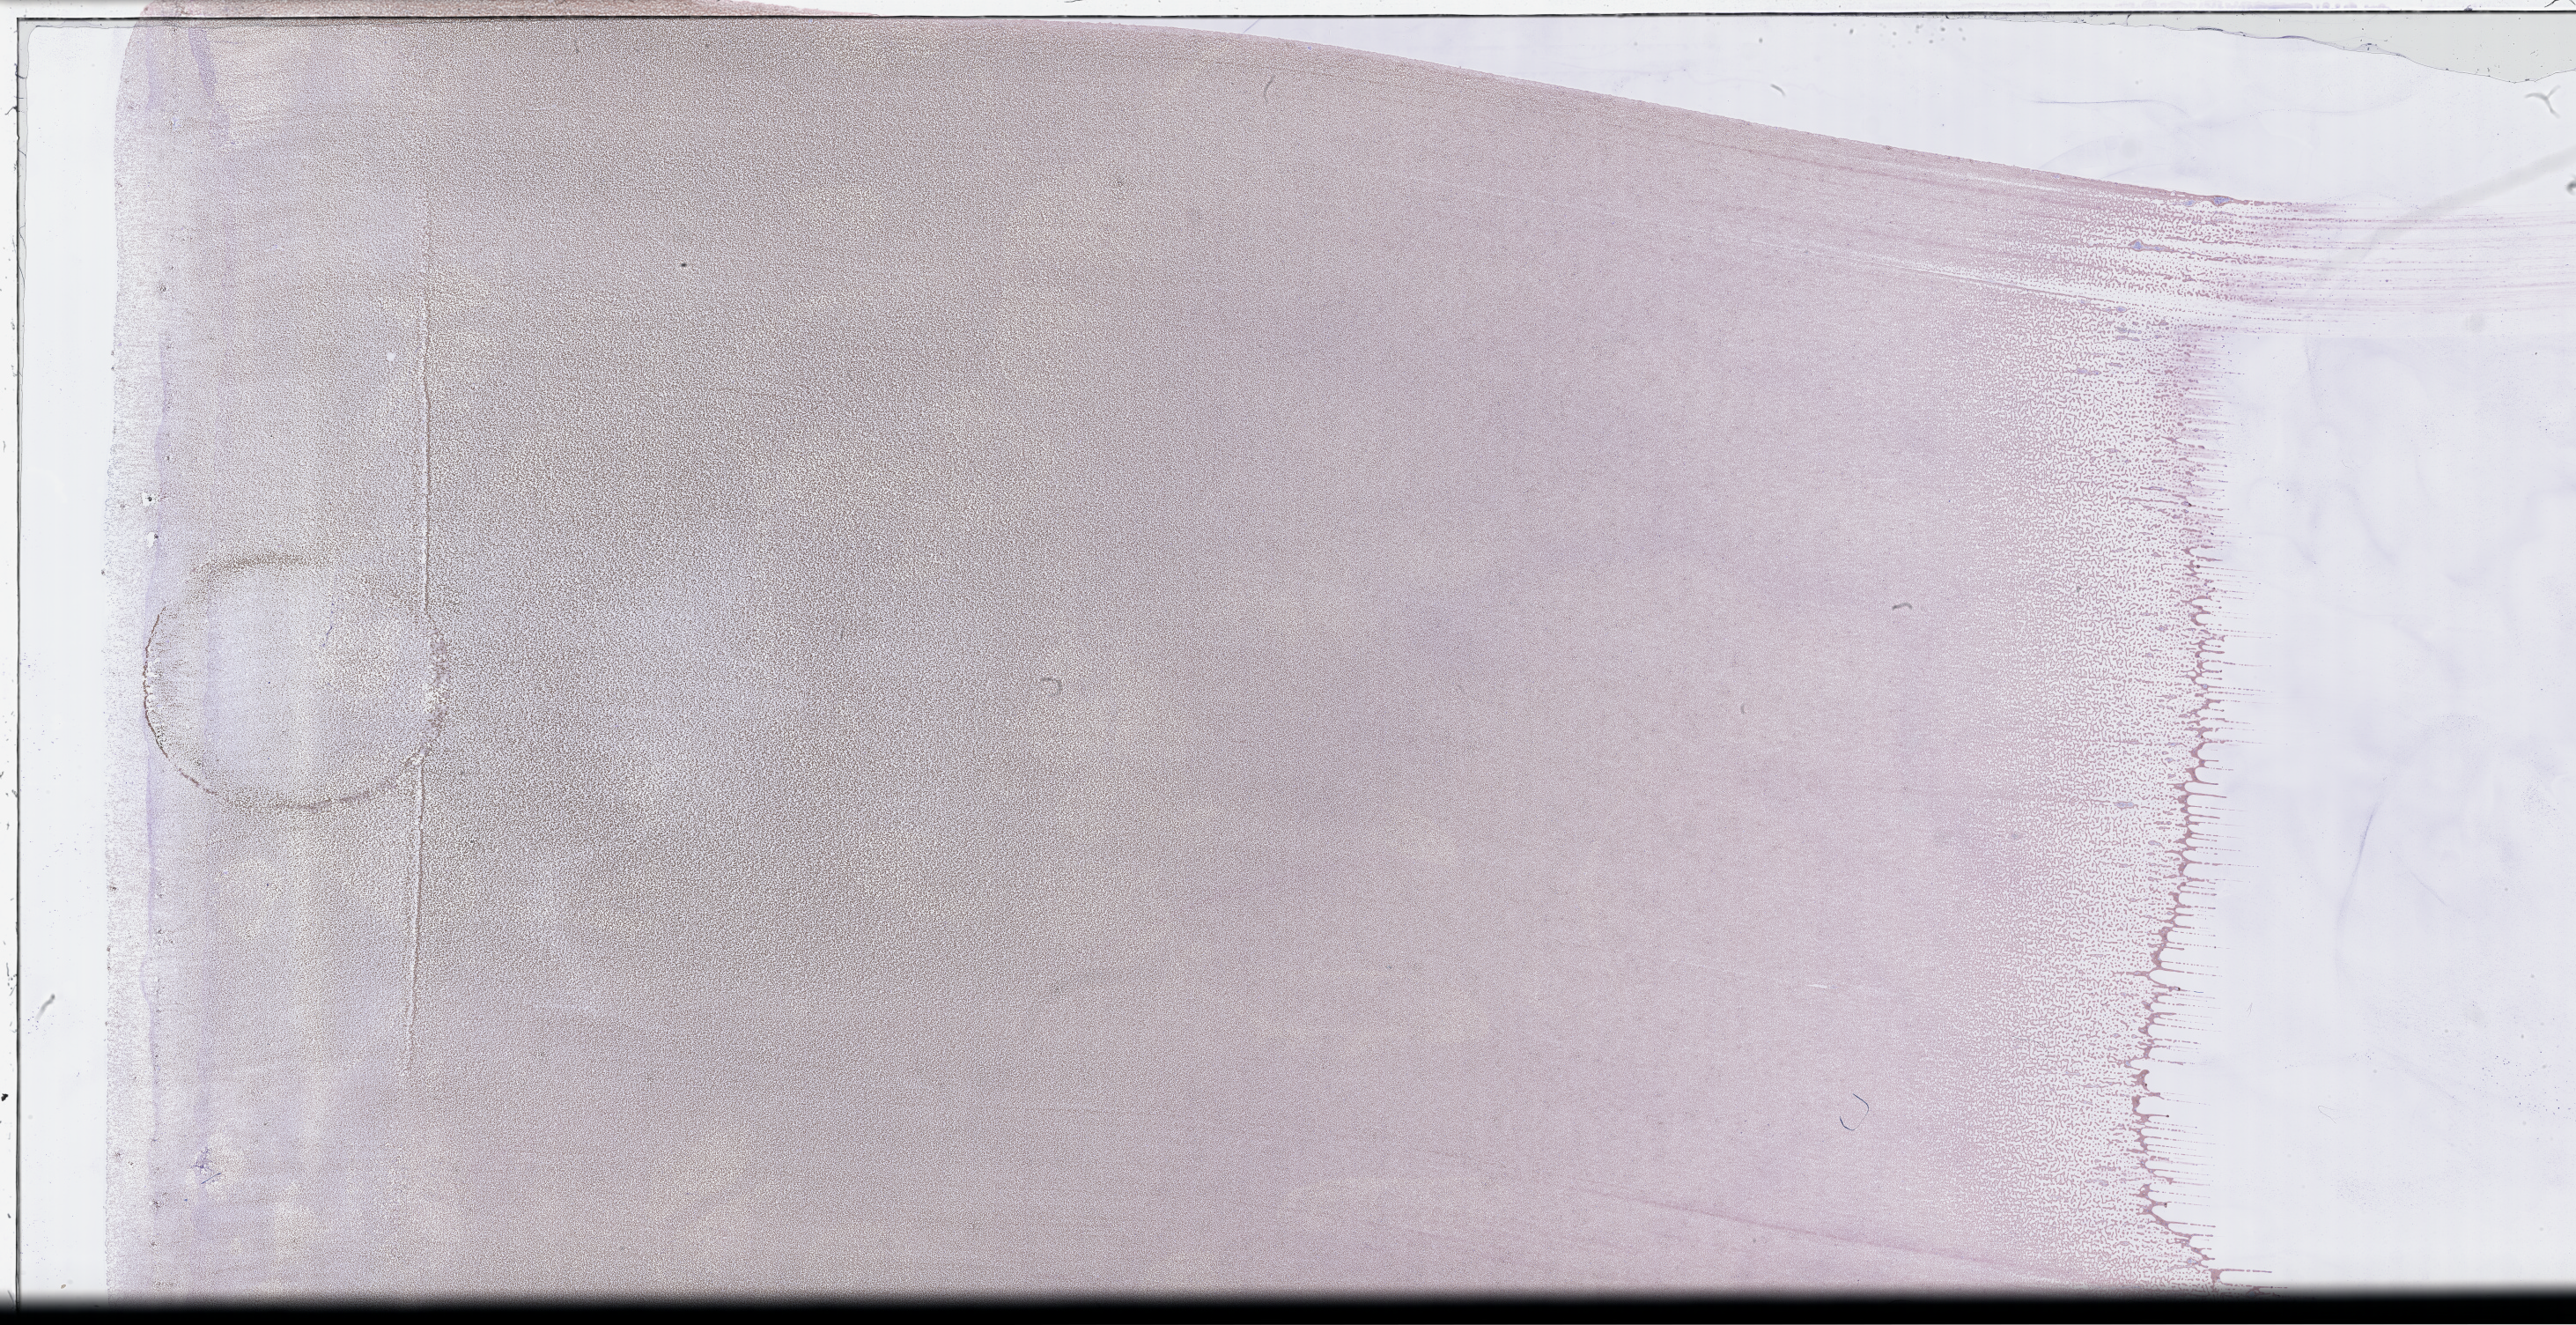
Wright–Giemsa-stained whole blood smear, whole-slide image, a low-resolution overview of the entire scanned area, about 47.2 x 24.3 mm; smear from an EDTA sample; collected at baseline (before treatment). Patient sex: male.
Patient diagnosis: Plasma Cell Myeloma.